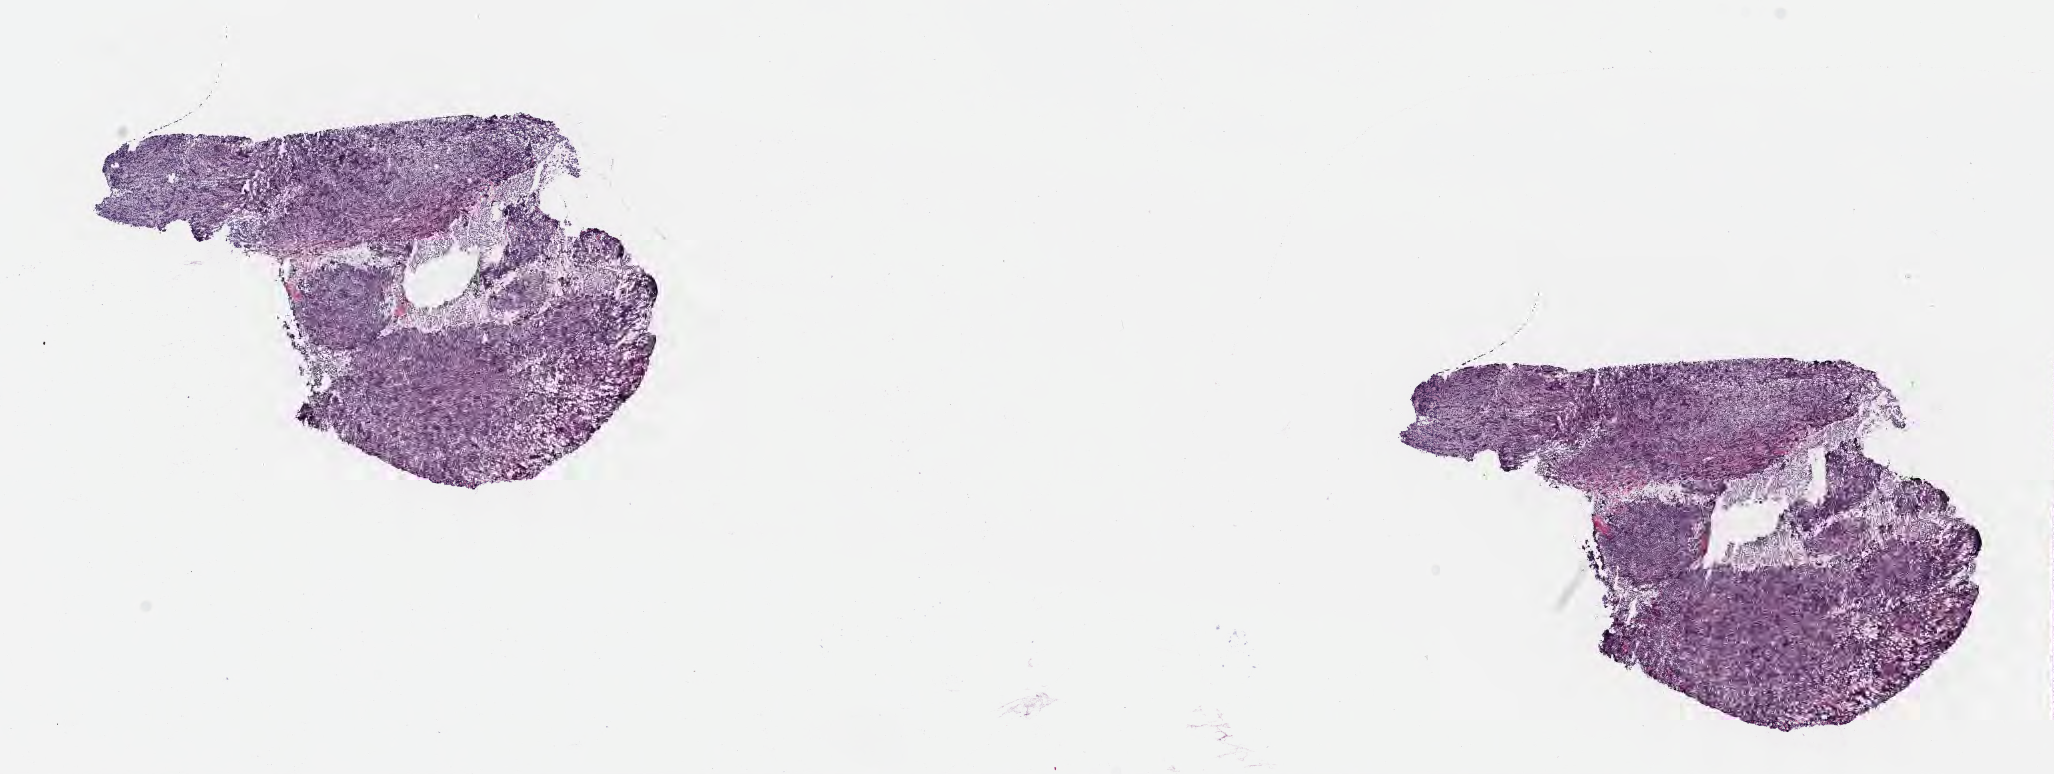
Digitized haematoxylin and eosin-stained section, low-resolution overview of the scanned area, about 16.6 x 6.3 mm, cryosection, specimen: primary tumor, site: cranium. Patient: male, age at initial diagnosis 2 years. Composition of this section per pathologist review: tumor cells 80%, tumor nuclei 85%, stromal cells 10%, necrosis 5%, normal cells 5%. Infiltration values recorded for this section: lymphocyte infiltration 45%, monocyte infiltration 30%, neutrophil infiltration 5%.
- Ann Arbor stage (patient): Stage IV
- diagnosis: Burkitt lymphoma, NOS
- section: top of the tissue portion